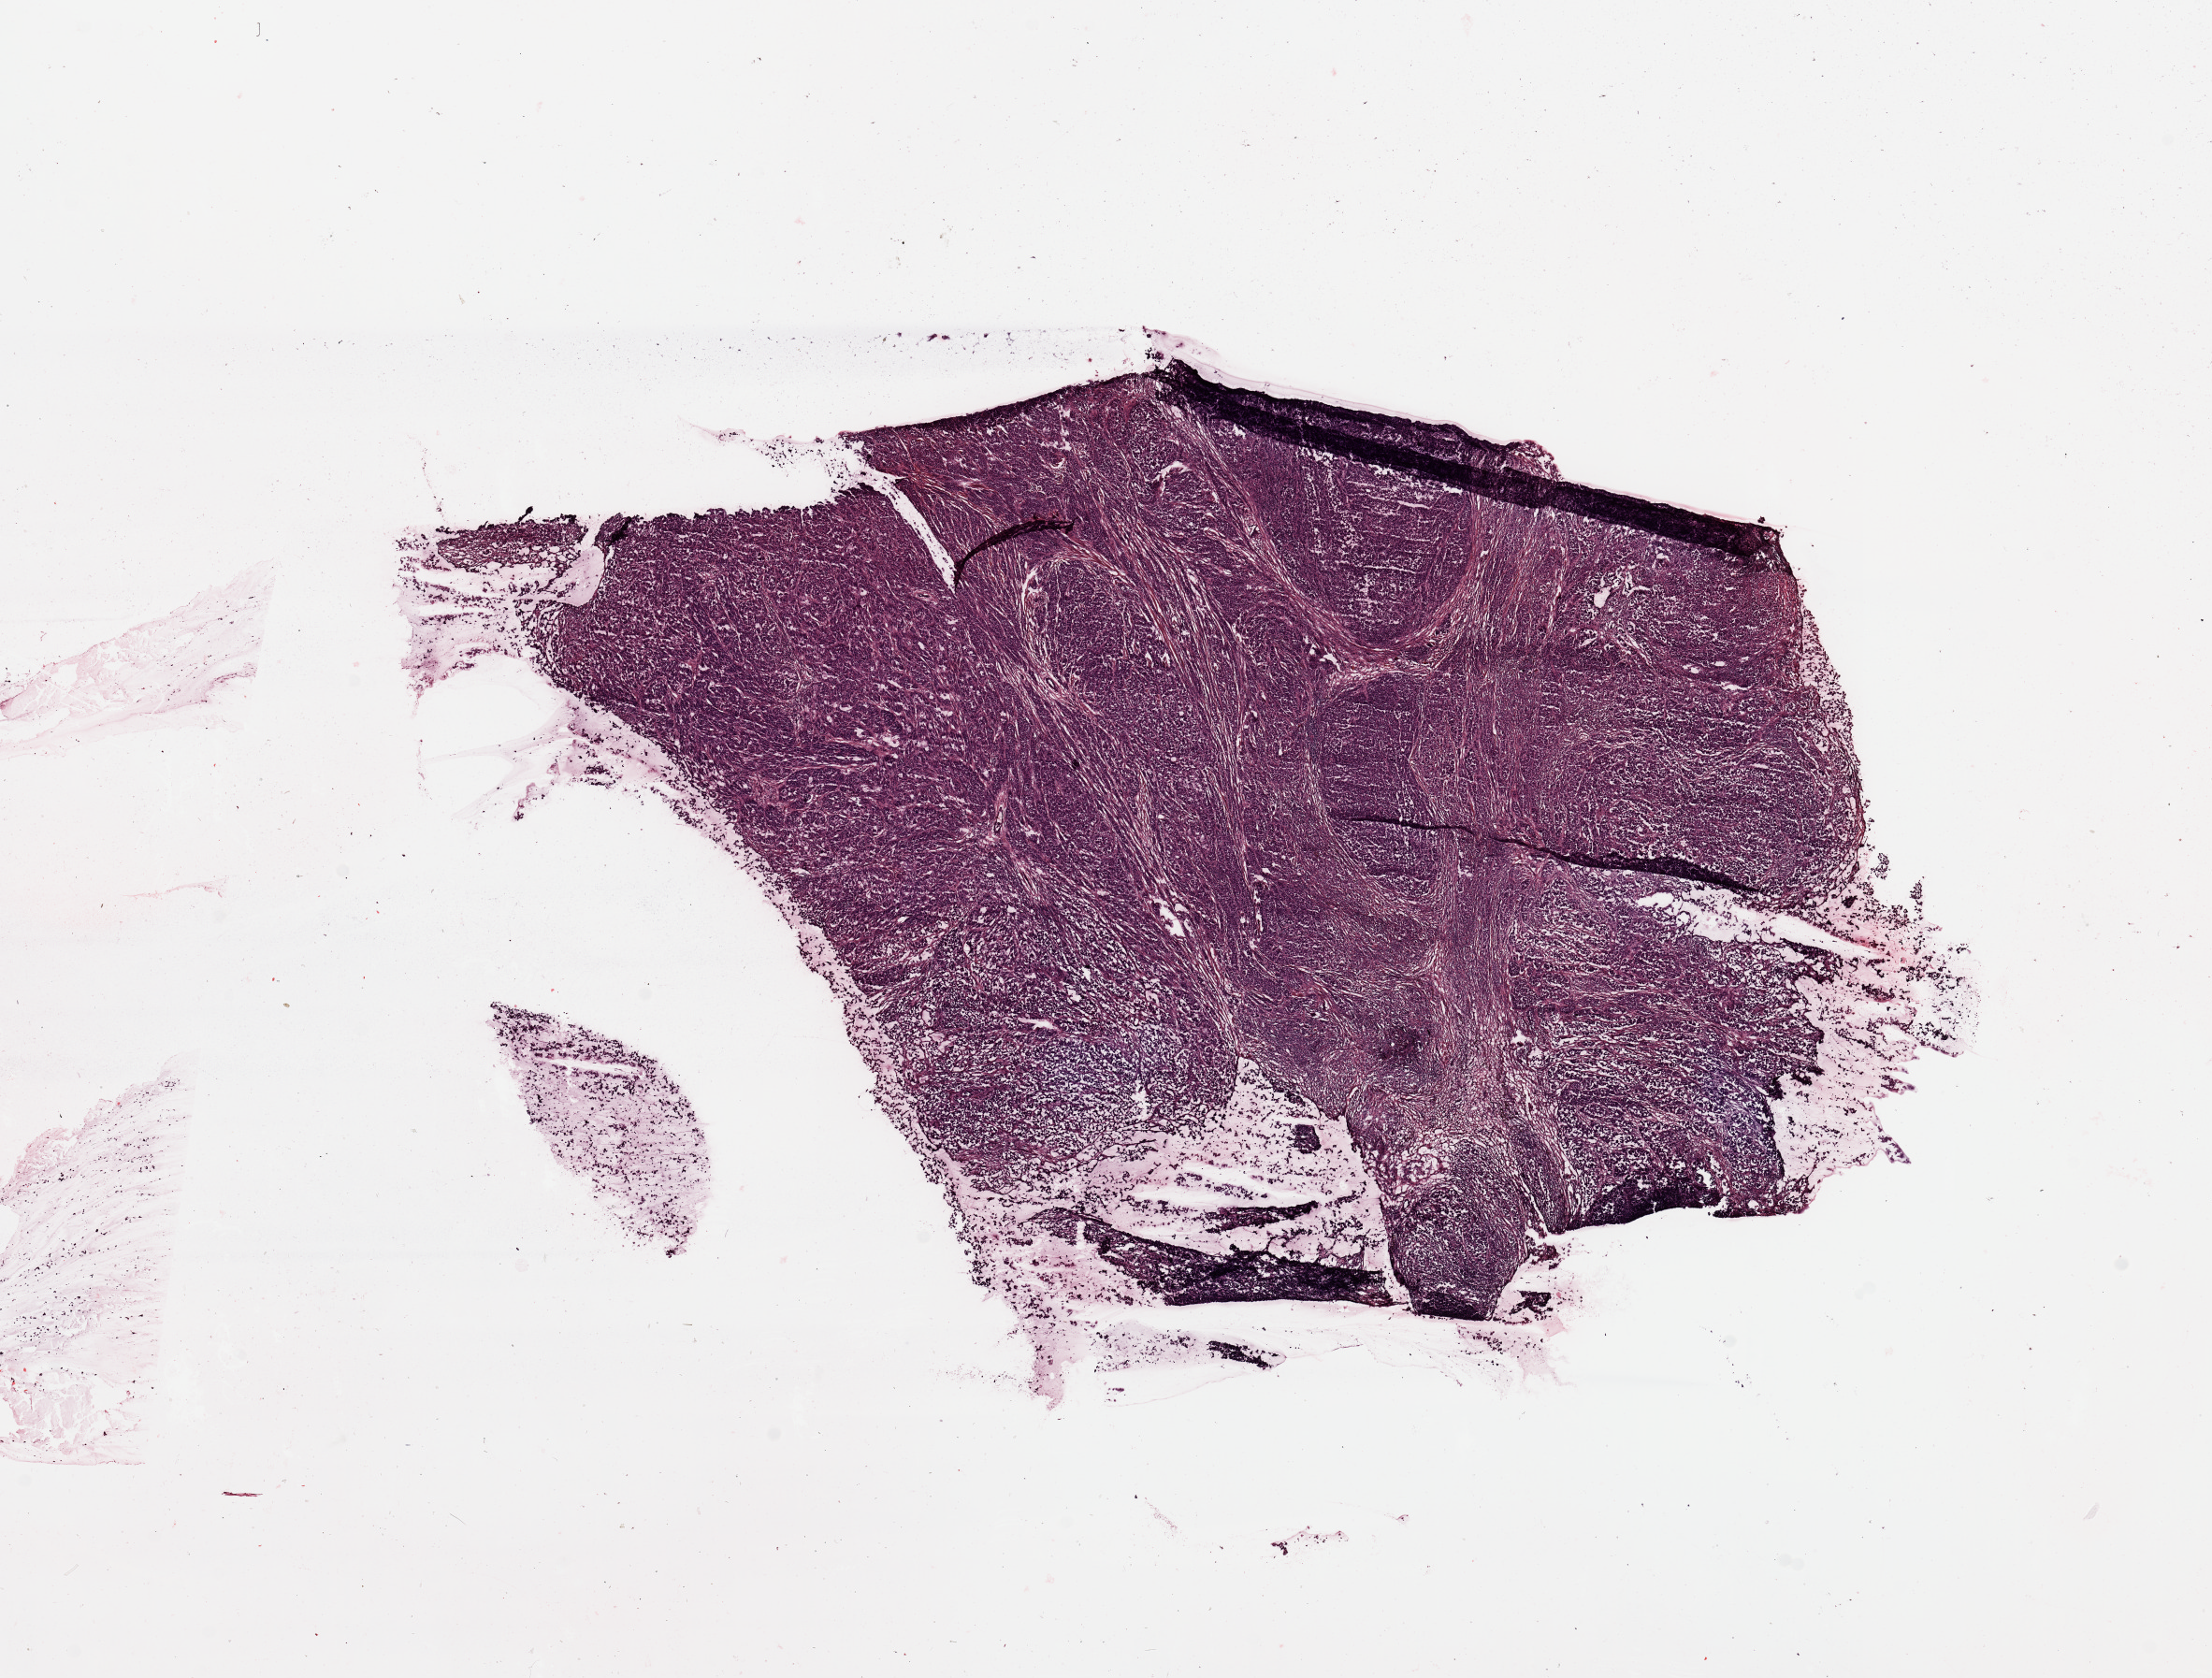
Digitized Hematoxylin and eosin (H&E) stained tissue section (whole slide), a low-resolution overview of the entire scanned area, about 18.7 x 14.2 mm, melanoma tumour tissue; sampled site not recorded. Female, 51 y/o.
Patient diagnosis (cohort enrolment): cutaneous melanoma (skin). Primary tumour site (as recorded): extremities.